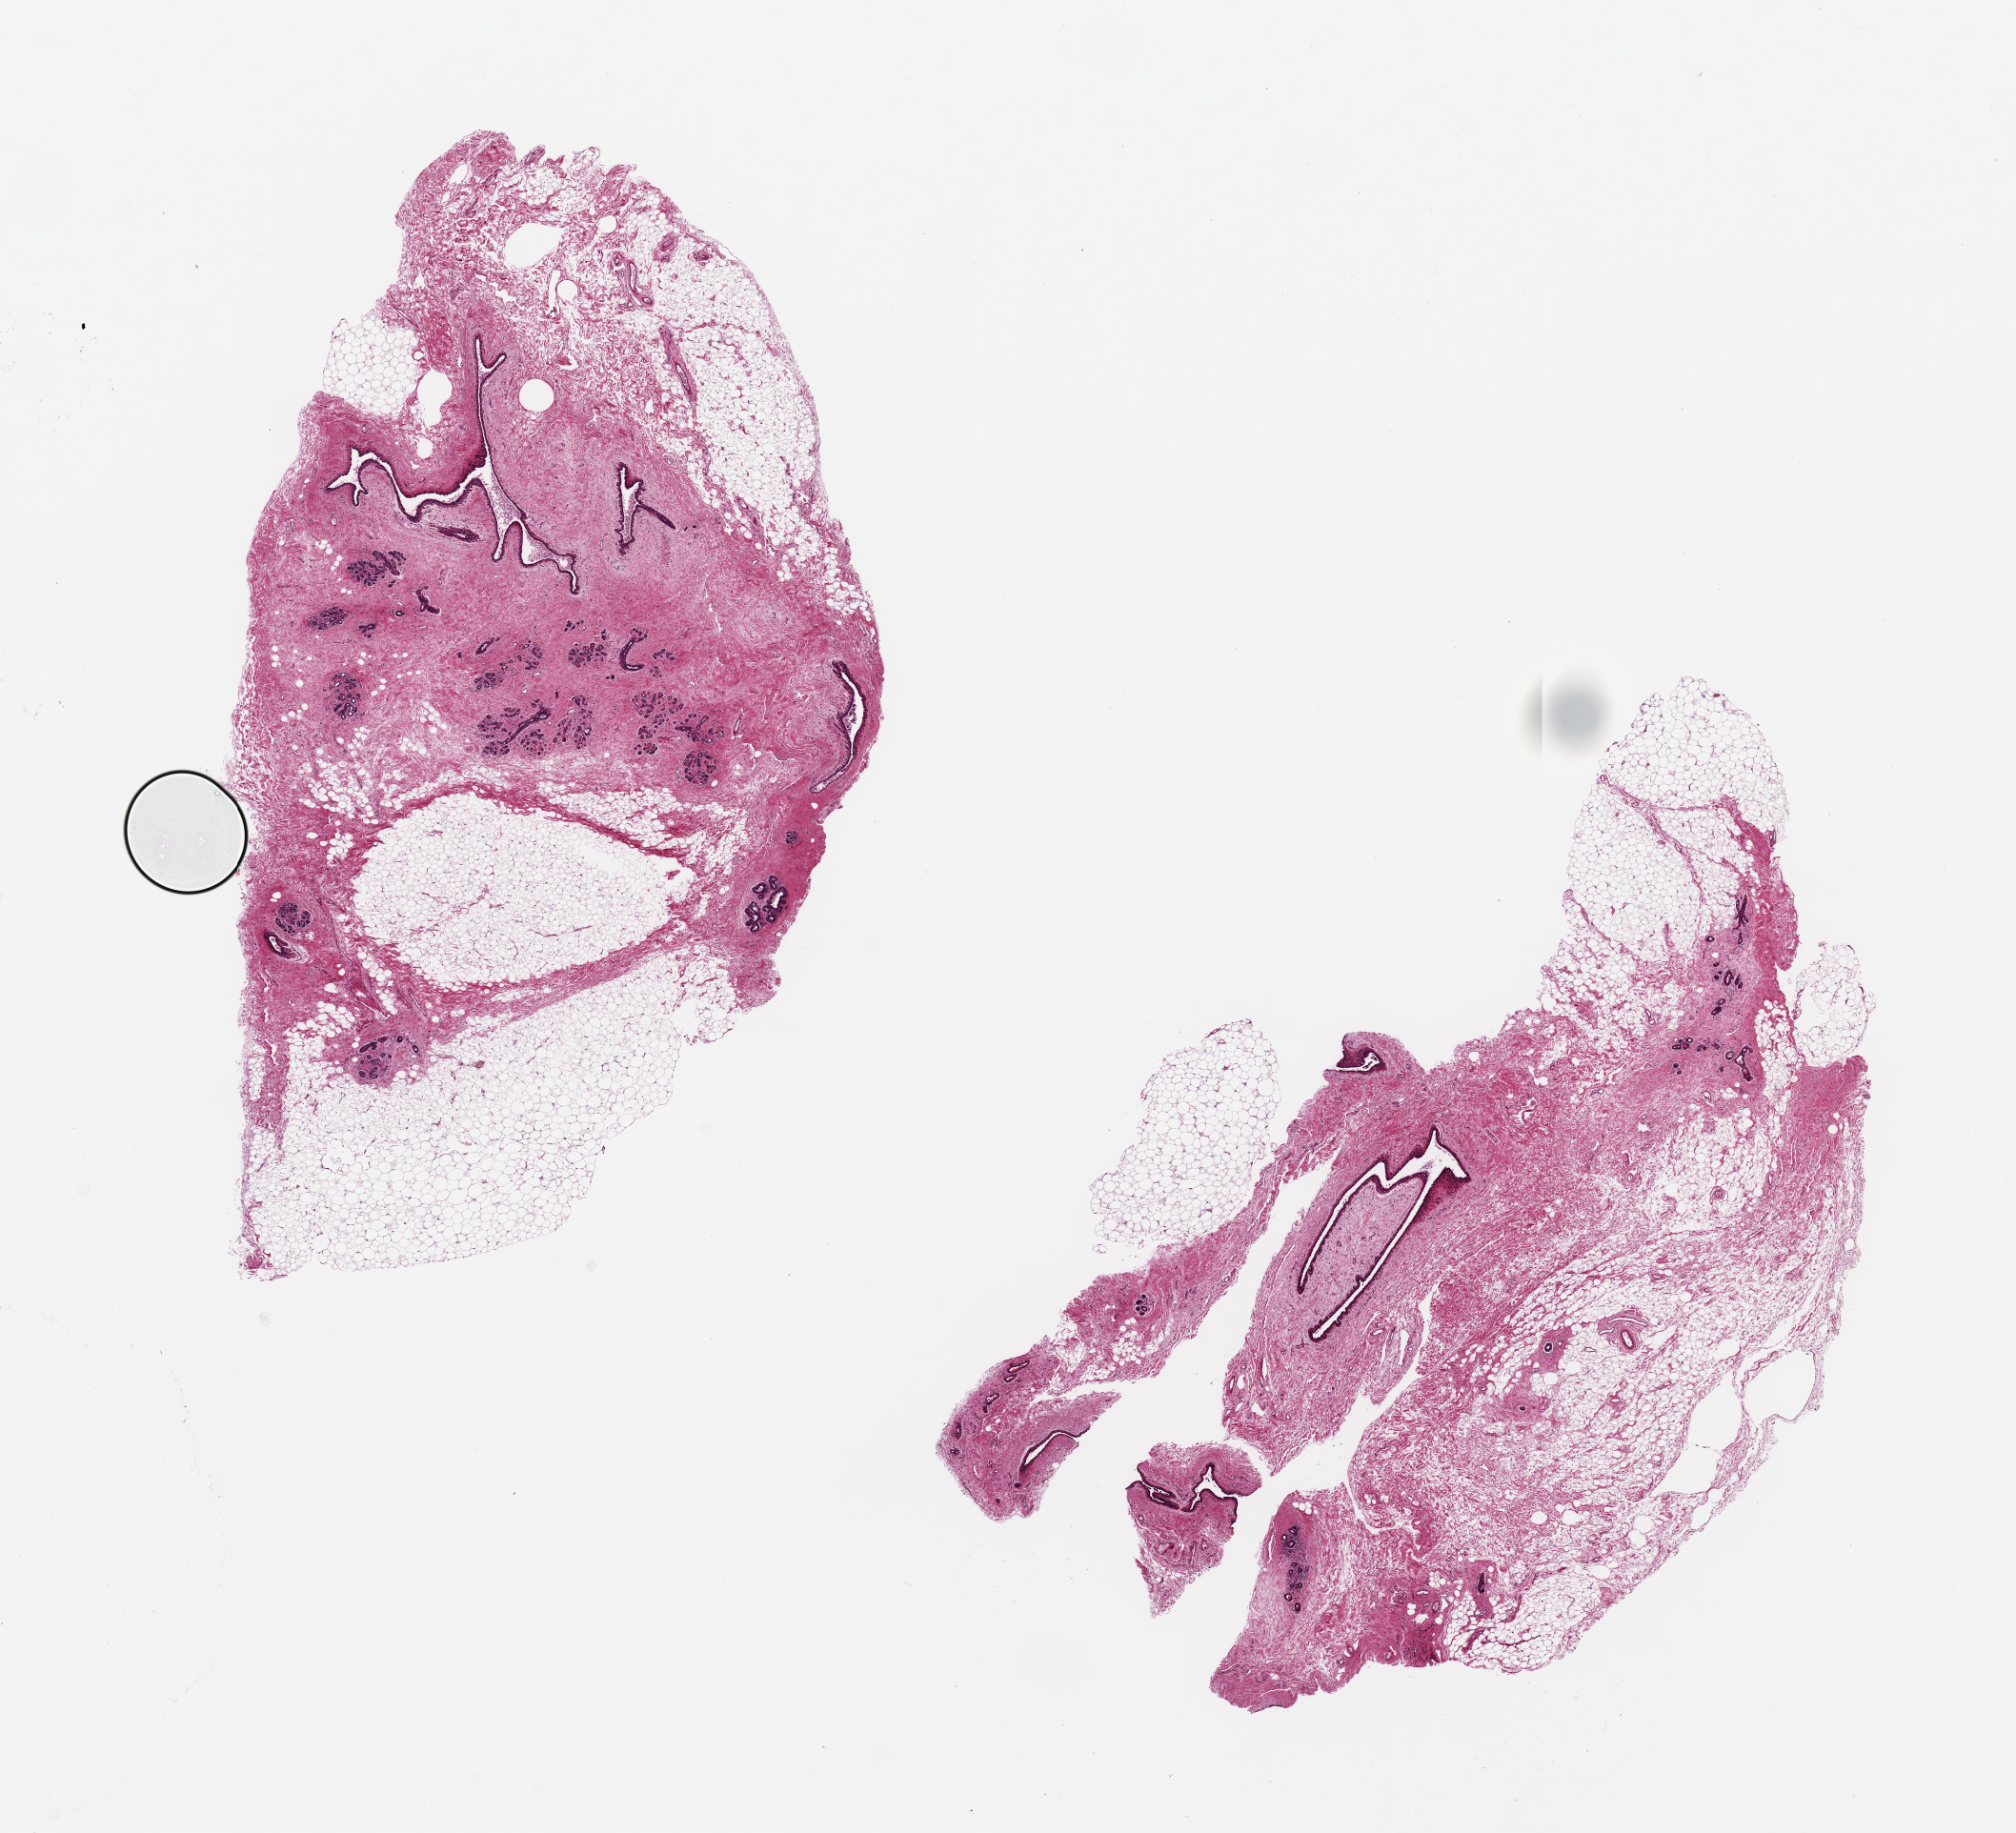
Whole-slide image, hematoxylin and eosin (H&E) stain, shown as a low-resolution overview of the whole scanned area (about 16.7 x 15.2 mm), PAXgene-fixed, paraffin-embedded tissue, sampled site (target tissue): breast, tissue donor sample. Donor: female.
- review note (as recorded): 2pieces ~9x5mm; TDLUs evident